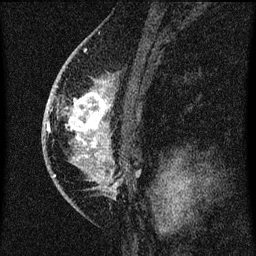
Breast MRI (dynamic contrast-enhanced), one sagittal slice. Position 43 of 60 along the scan axis. Dynamic contrast-enhanced series, image 2 of 3 at this slice position (ordered by acquisition). 1.5 T. TE 4.2 ms, TR 8 ms. 2 mm slice thickness. 256 × 256 image matrix, field of view 180 × 180 mm. Female patient, age 46 years.
Structures marked on this image (semi-automatically segmented with operator editing):
- analysis volume of interest (the breast-tissue region the enhancement analysis was run in; not a lesion): bounding box (x1, y1, x2, y2) in pixels: (54, 68, 115, 195)
- tumour enhancement mask (voxels above the 70 % enhancement threshold inside the analysis volume of interest): (66, 82, 110, 179)